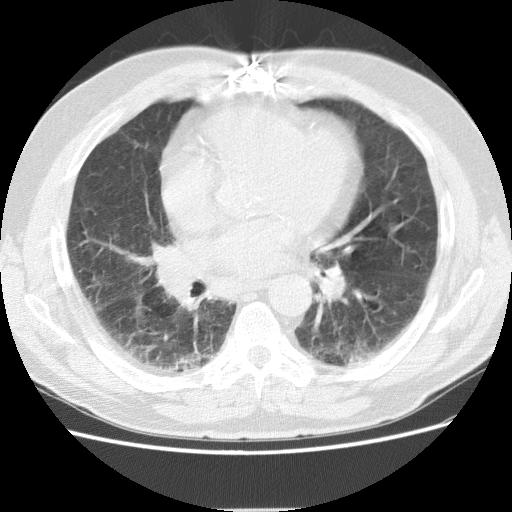
Axial slice from a low-dose chest CT screening exam, baseline annual screen, lung window (W 1500 / L -600 HU), standard (soft-tissue) reconstruction kernel (STANDARD), slice 69 of 155 in the series. Male, age 72 years at enrolment.
- Expert-annotated lung lesion, bounding box <147,235,195,272> (left, top, right, bottom; pixels).
- Screening reader's record for this exam: no non-calcified nodule ≥4 mm recorded.
- Participant outcome: lung cancer diagnosed 163 days after this screen — adenocarcinoma, NOS, right middle lobe, stage IIIB (AJCC 6th edition), 27 mm at pathology.